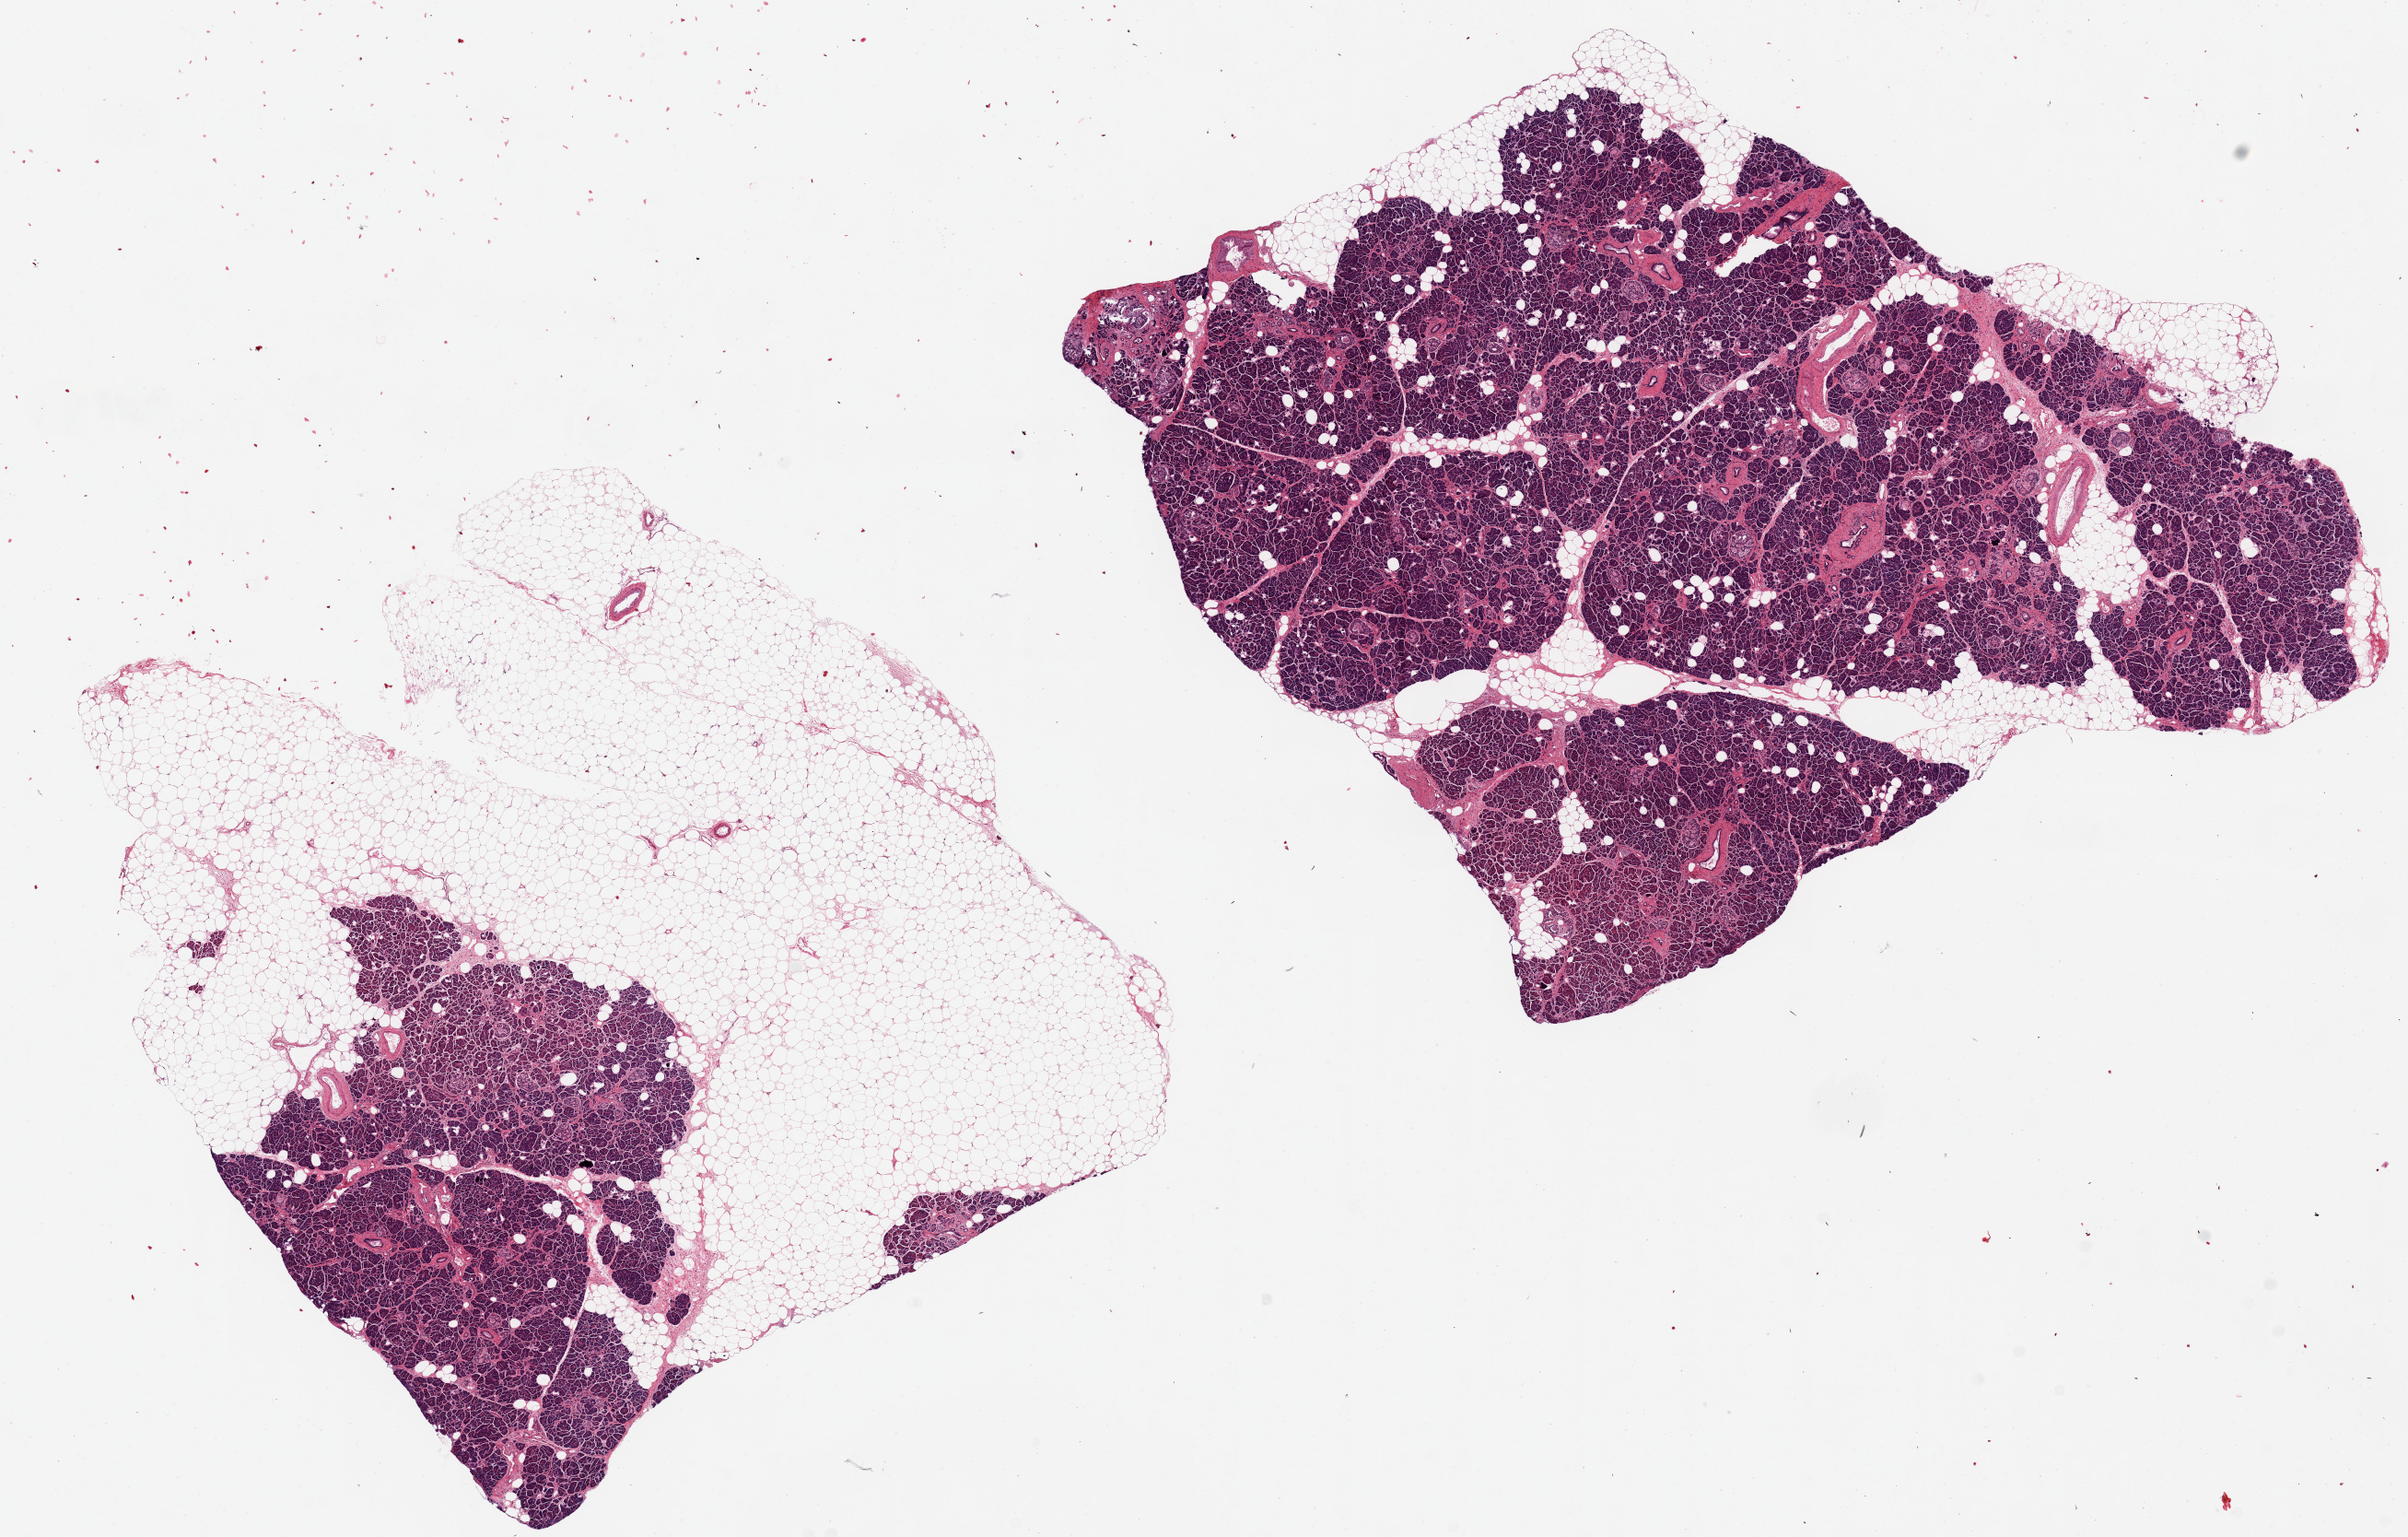
Hematoxylin and eosin (H&E) whole-slide image, brightfield — low-resolution overview of the scanned area, about 20.7 x 13.2 mm. PAXgene-fixed paraffin-embedded (PFPE) section. Section of pancreas (target tissue). Tissue donor sample. Male donor.
- review note (as recorded): 2 pieces ~8x7mm well preserved, Islets well visualized, 30% of one aliquot is parenchyma, 90% of the other, both